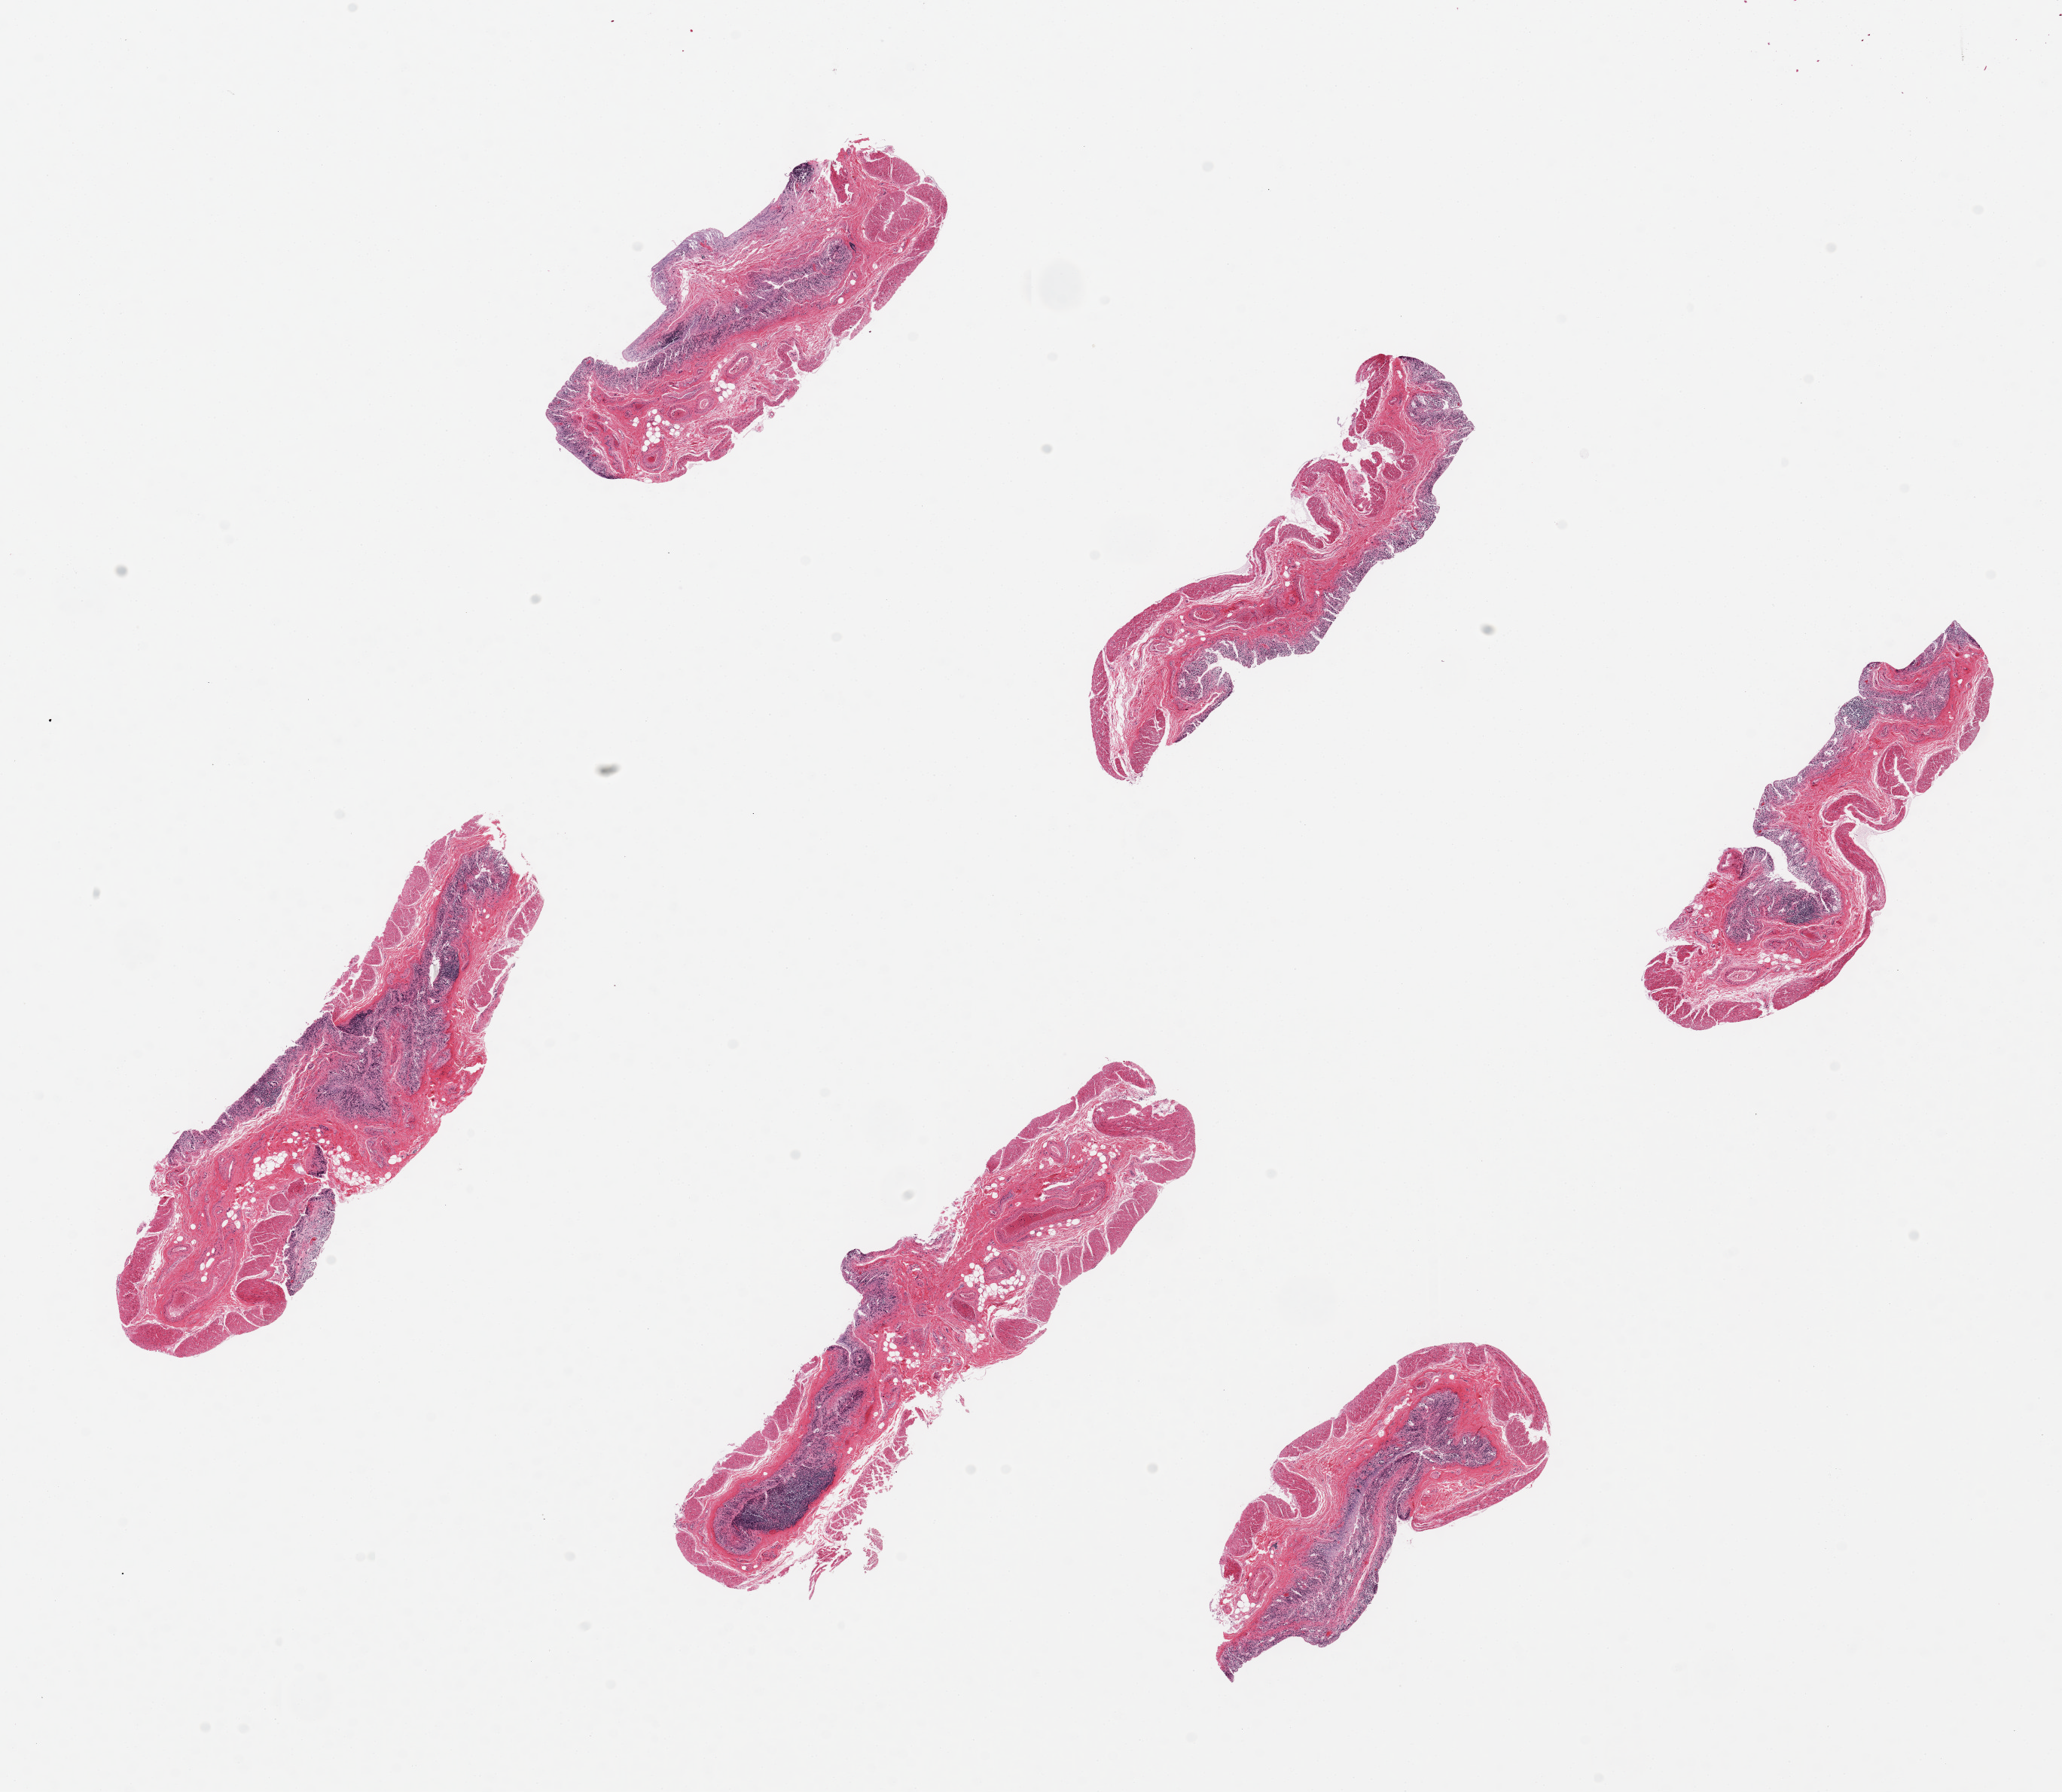
Whole-slide image, haematoxylin and eosin stain, shown as a low-resolution overview of the whole scanned area (about 21.7 x 18.8 mm, from a 20x scan). PAXgene-fixed paraffin-embedded (PFPE) section. Sampled site (target tissue): transverse colon. Donor tissue sample. Donor: male.
Reviewer comment on this tissue sample: 6 pieces up to 7x15 mm; glands completely sloughed.